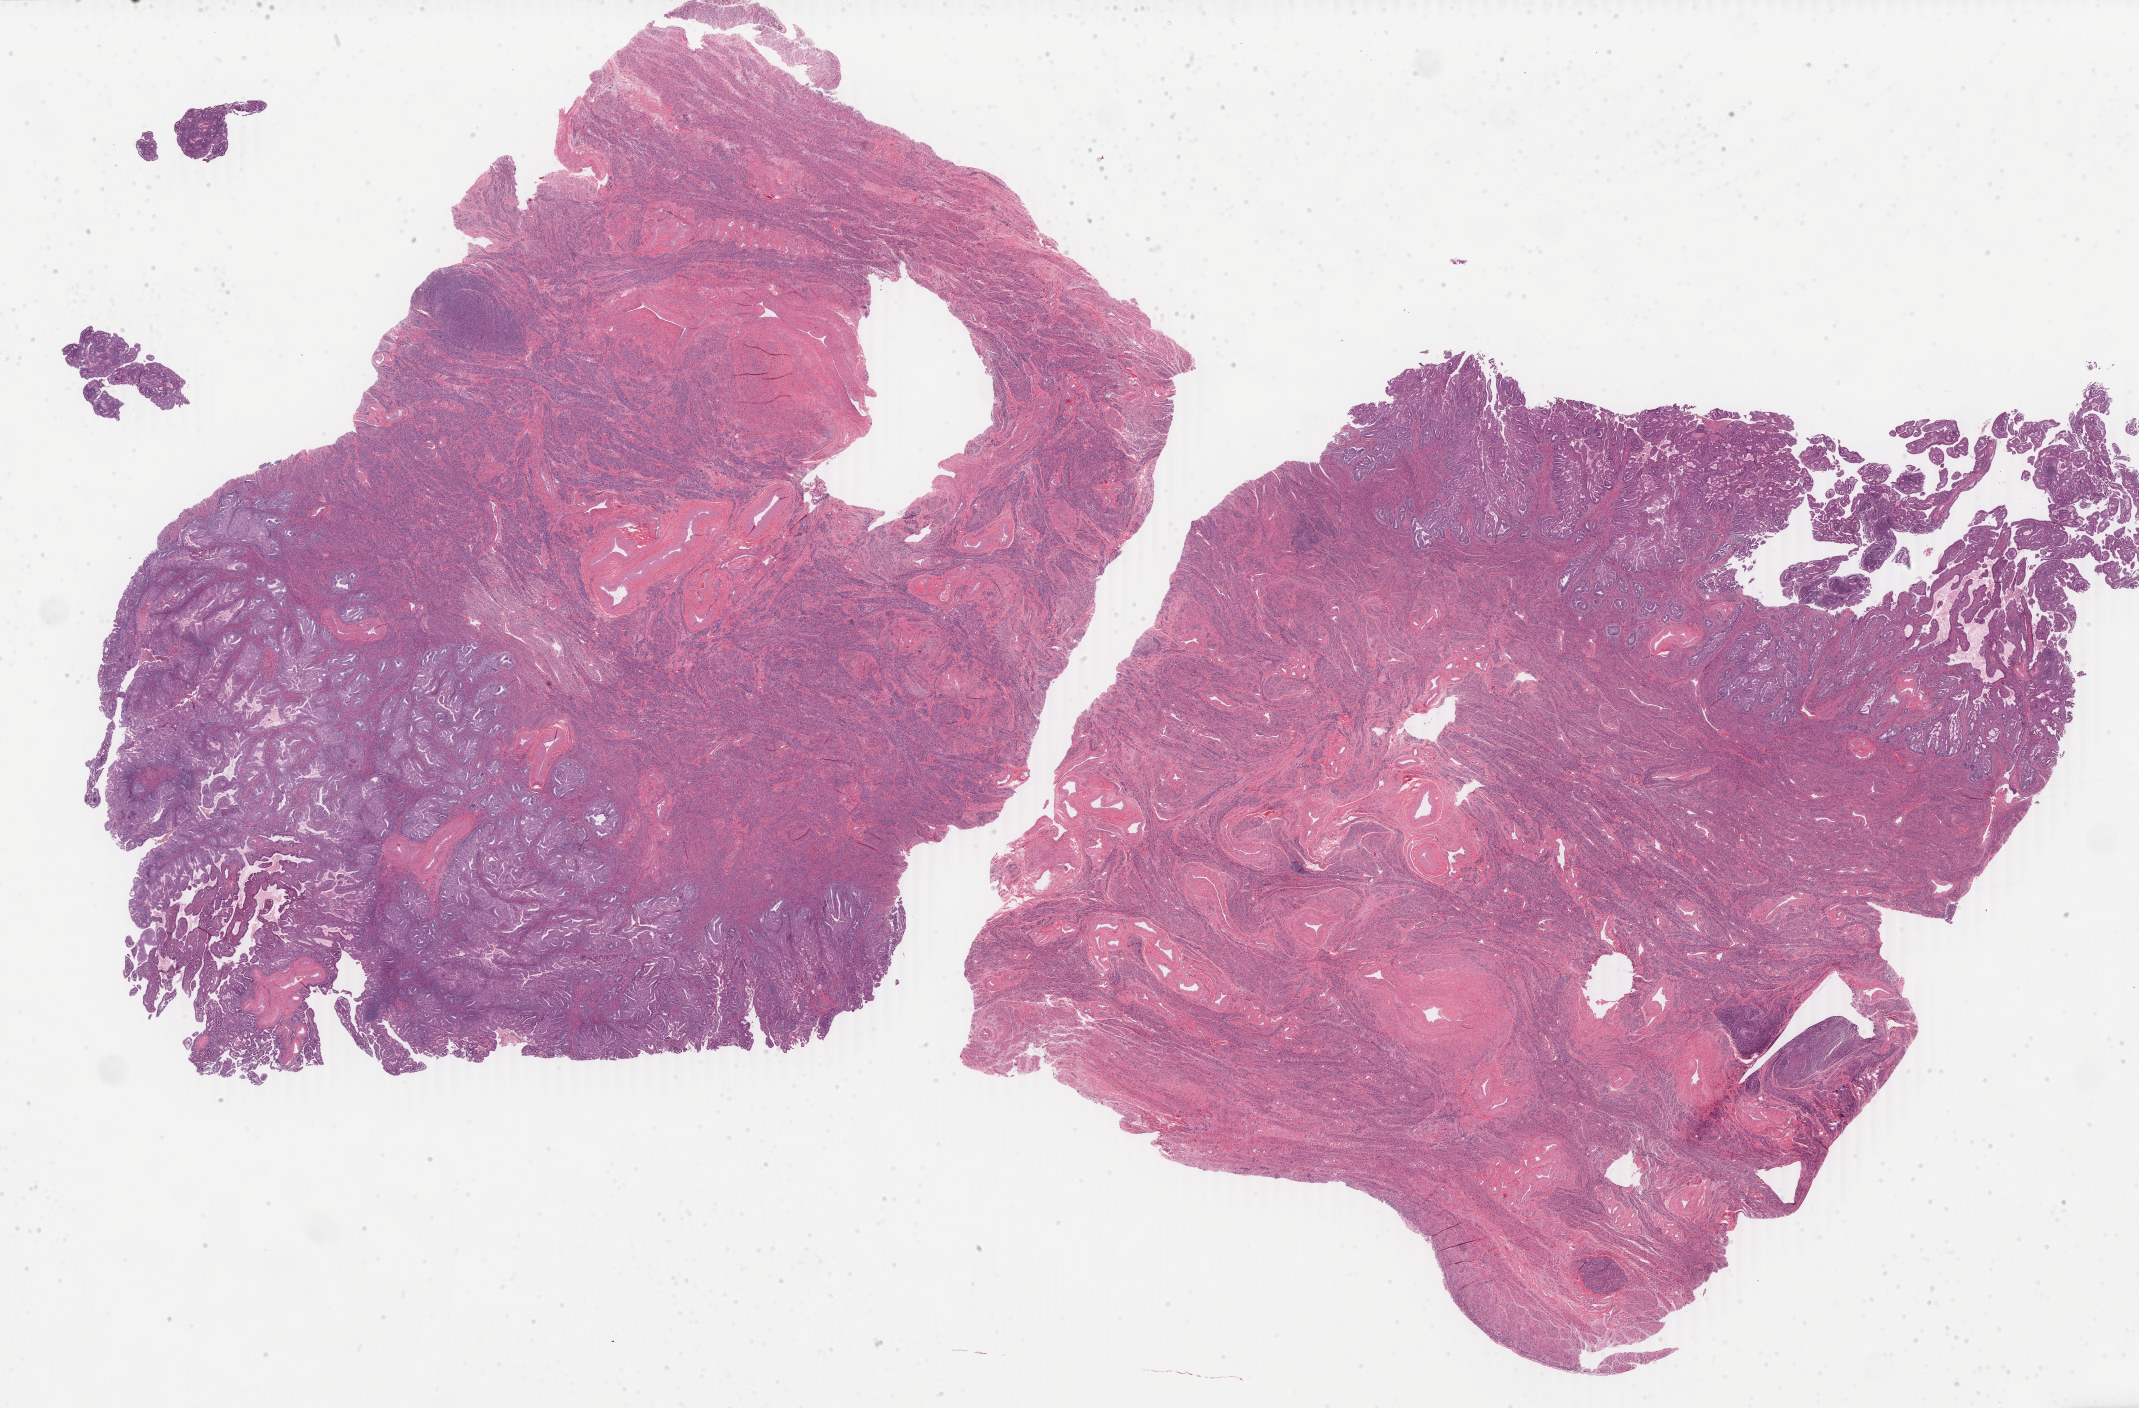
H&E-stained whole-slide image — shown as a low-resolution overview of the whole scanned area (about 34.0 x 22.4 mm, from a 40x scan); formalin-fixed paraffin-embedded (FFPE) diagnostic section; sample: primary tumour, uterus. Female, age 58 years at initial diagnosis. Histologic grade: G2 (moderately differentiated).
Histologic diagnosis: Endometrioid adenocarcinoma, NOS (endometrium). FIGO stage: IB.